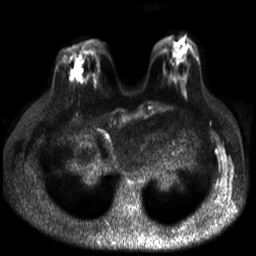
Breast MRI, one axial slice. Position 11 of 30 along the scan axis. Diffusion-weighted series; image 2 of 4 stored at this slice position (different b-values; order by instance number). 3 T. 4 mm slice thickness. 256 × 256 image matrix, field of view 320 × 320 mm. Female patient.
Annotated regions visible in this slice (expert manual segmentation):
- tumour on diffusion-weighted imaging: box from (x=70, y=67) to (x=81, y=81) px